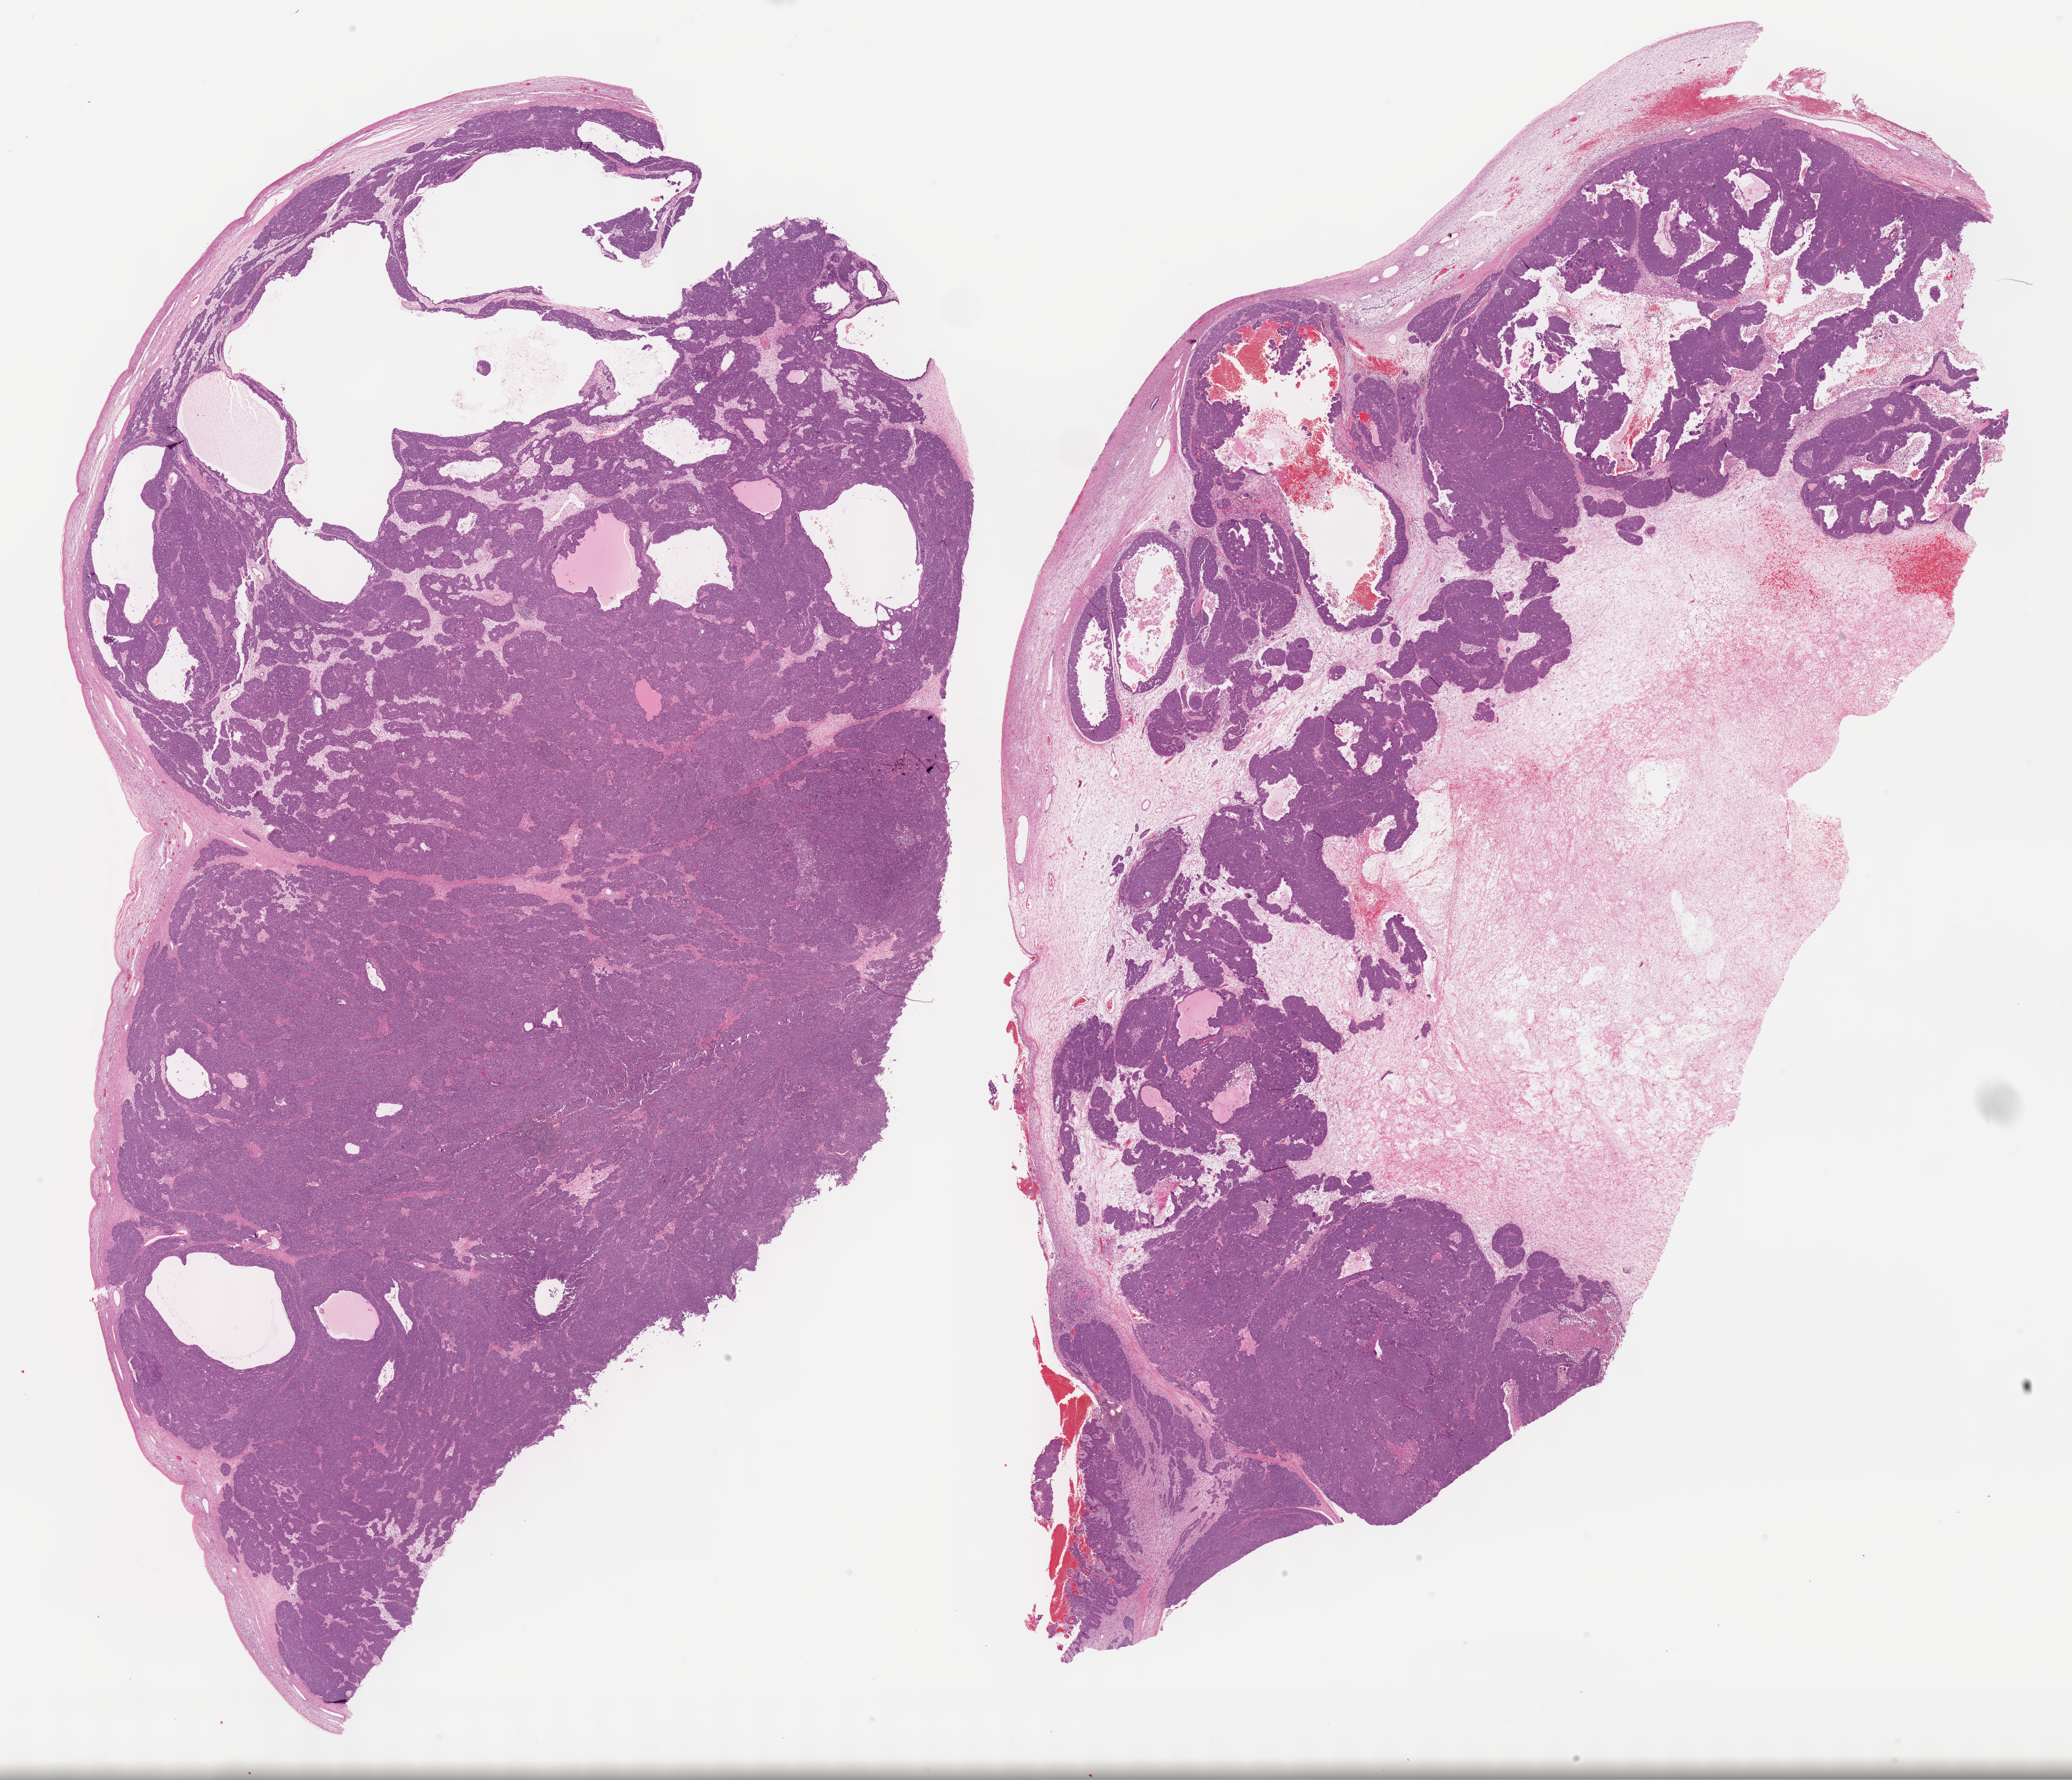
Whole-slide histology image, H&E-stained, shown as a low-resolution overview of the whole scanned area (about 25.2 x 21.6 mm), FFPE section, primary tumour sample from the ovary. Female, age 46 years at initial diagnosis. Histologic grade: G3 (poorly differentiated).
Pathologic diagnosis: Serous cystadenocarcinoma, NOS. FIGO stage: IIIC.